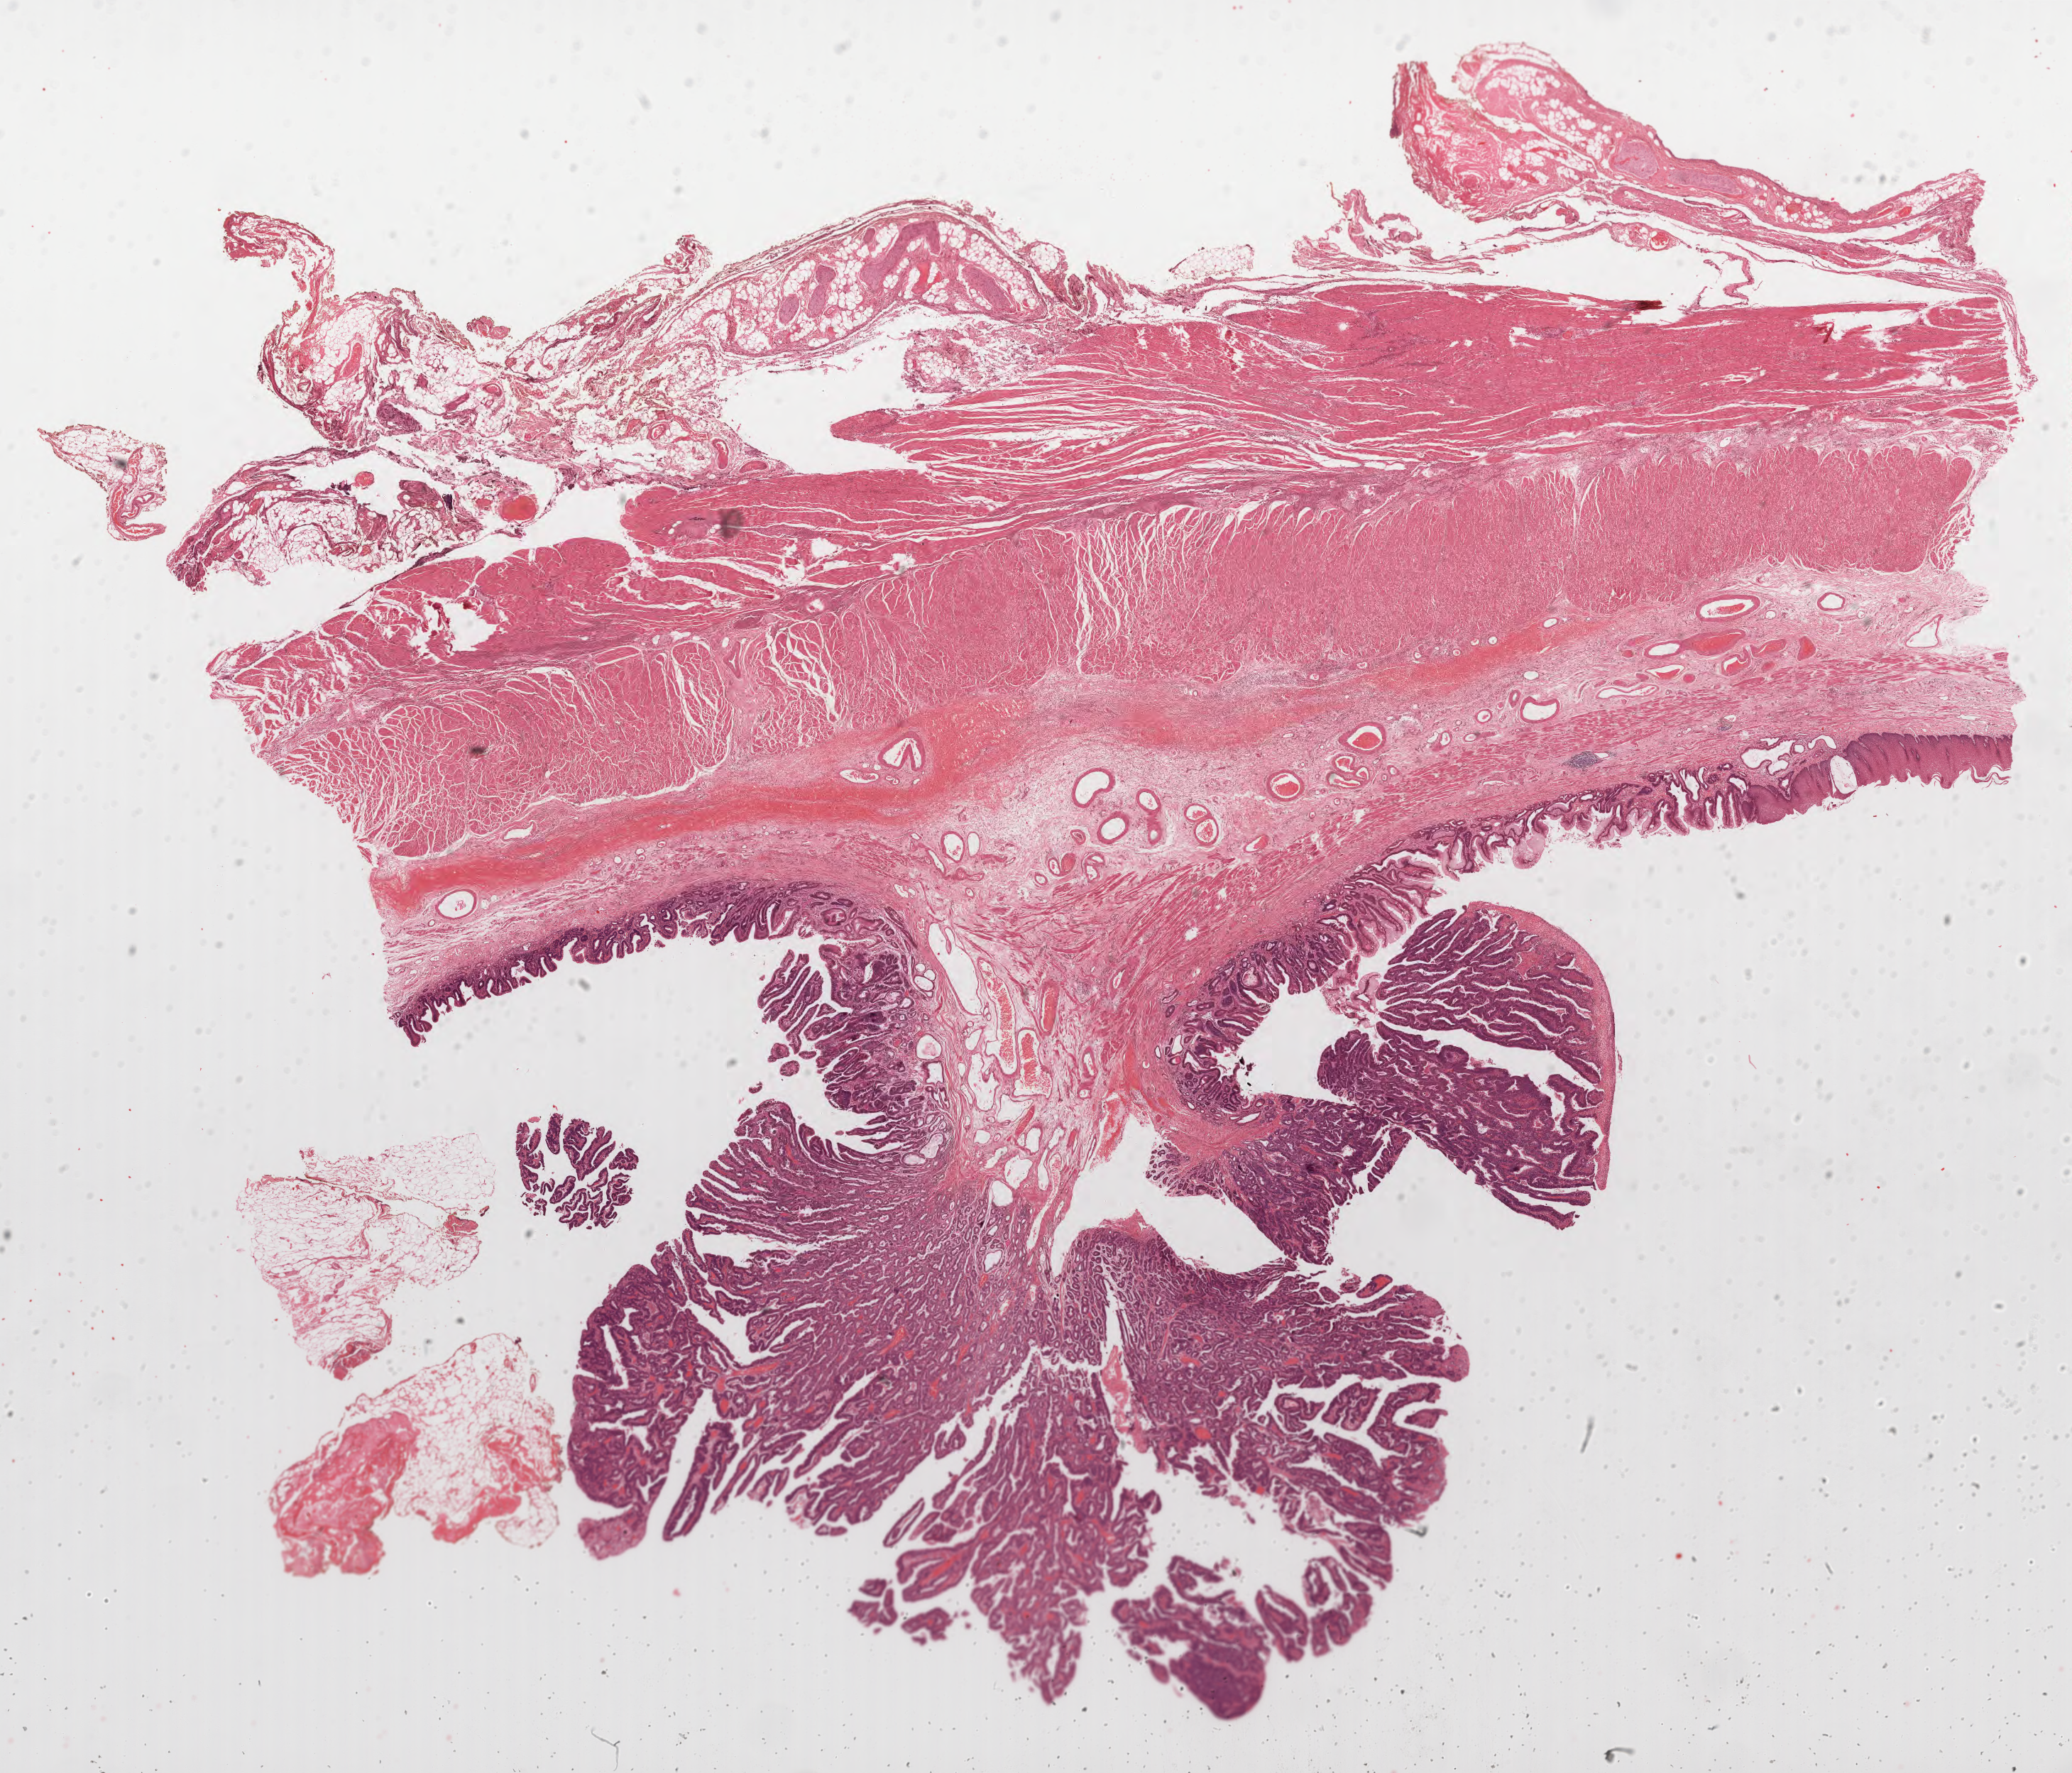
Digitized H&E-stained tissue section (whole slide) — low-resolution overview of the scanned area, about 23.5 x 20.1 mm (slide scanned at 40x), formalin-fixed paraffin-embedded (FFPE) diagnostic section, sample: primary tumour, esophagus. Male patient; age at initial diagnosis 56 years. Histologic grade: G1 (well differentiated).
AJCC pathologic stage: I (6th edition). Histologic diagnosis: Adenocarcinoma, NOS. Lymph nodes positive (case pathology): 0 of 12 examined.